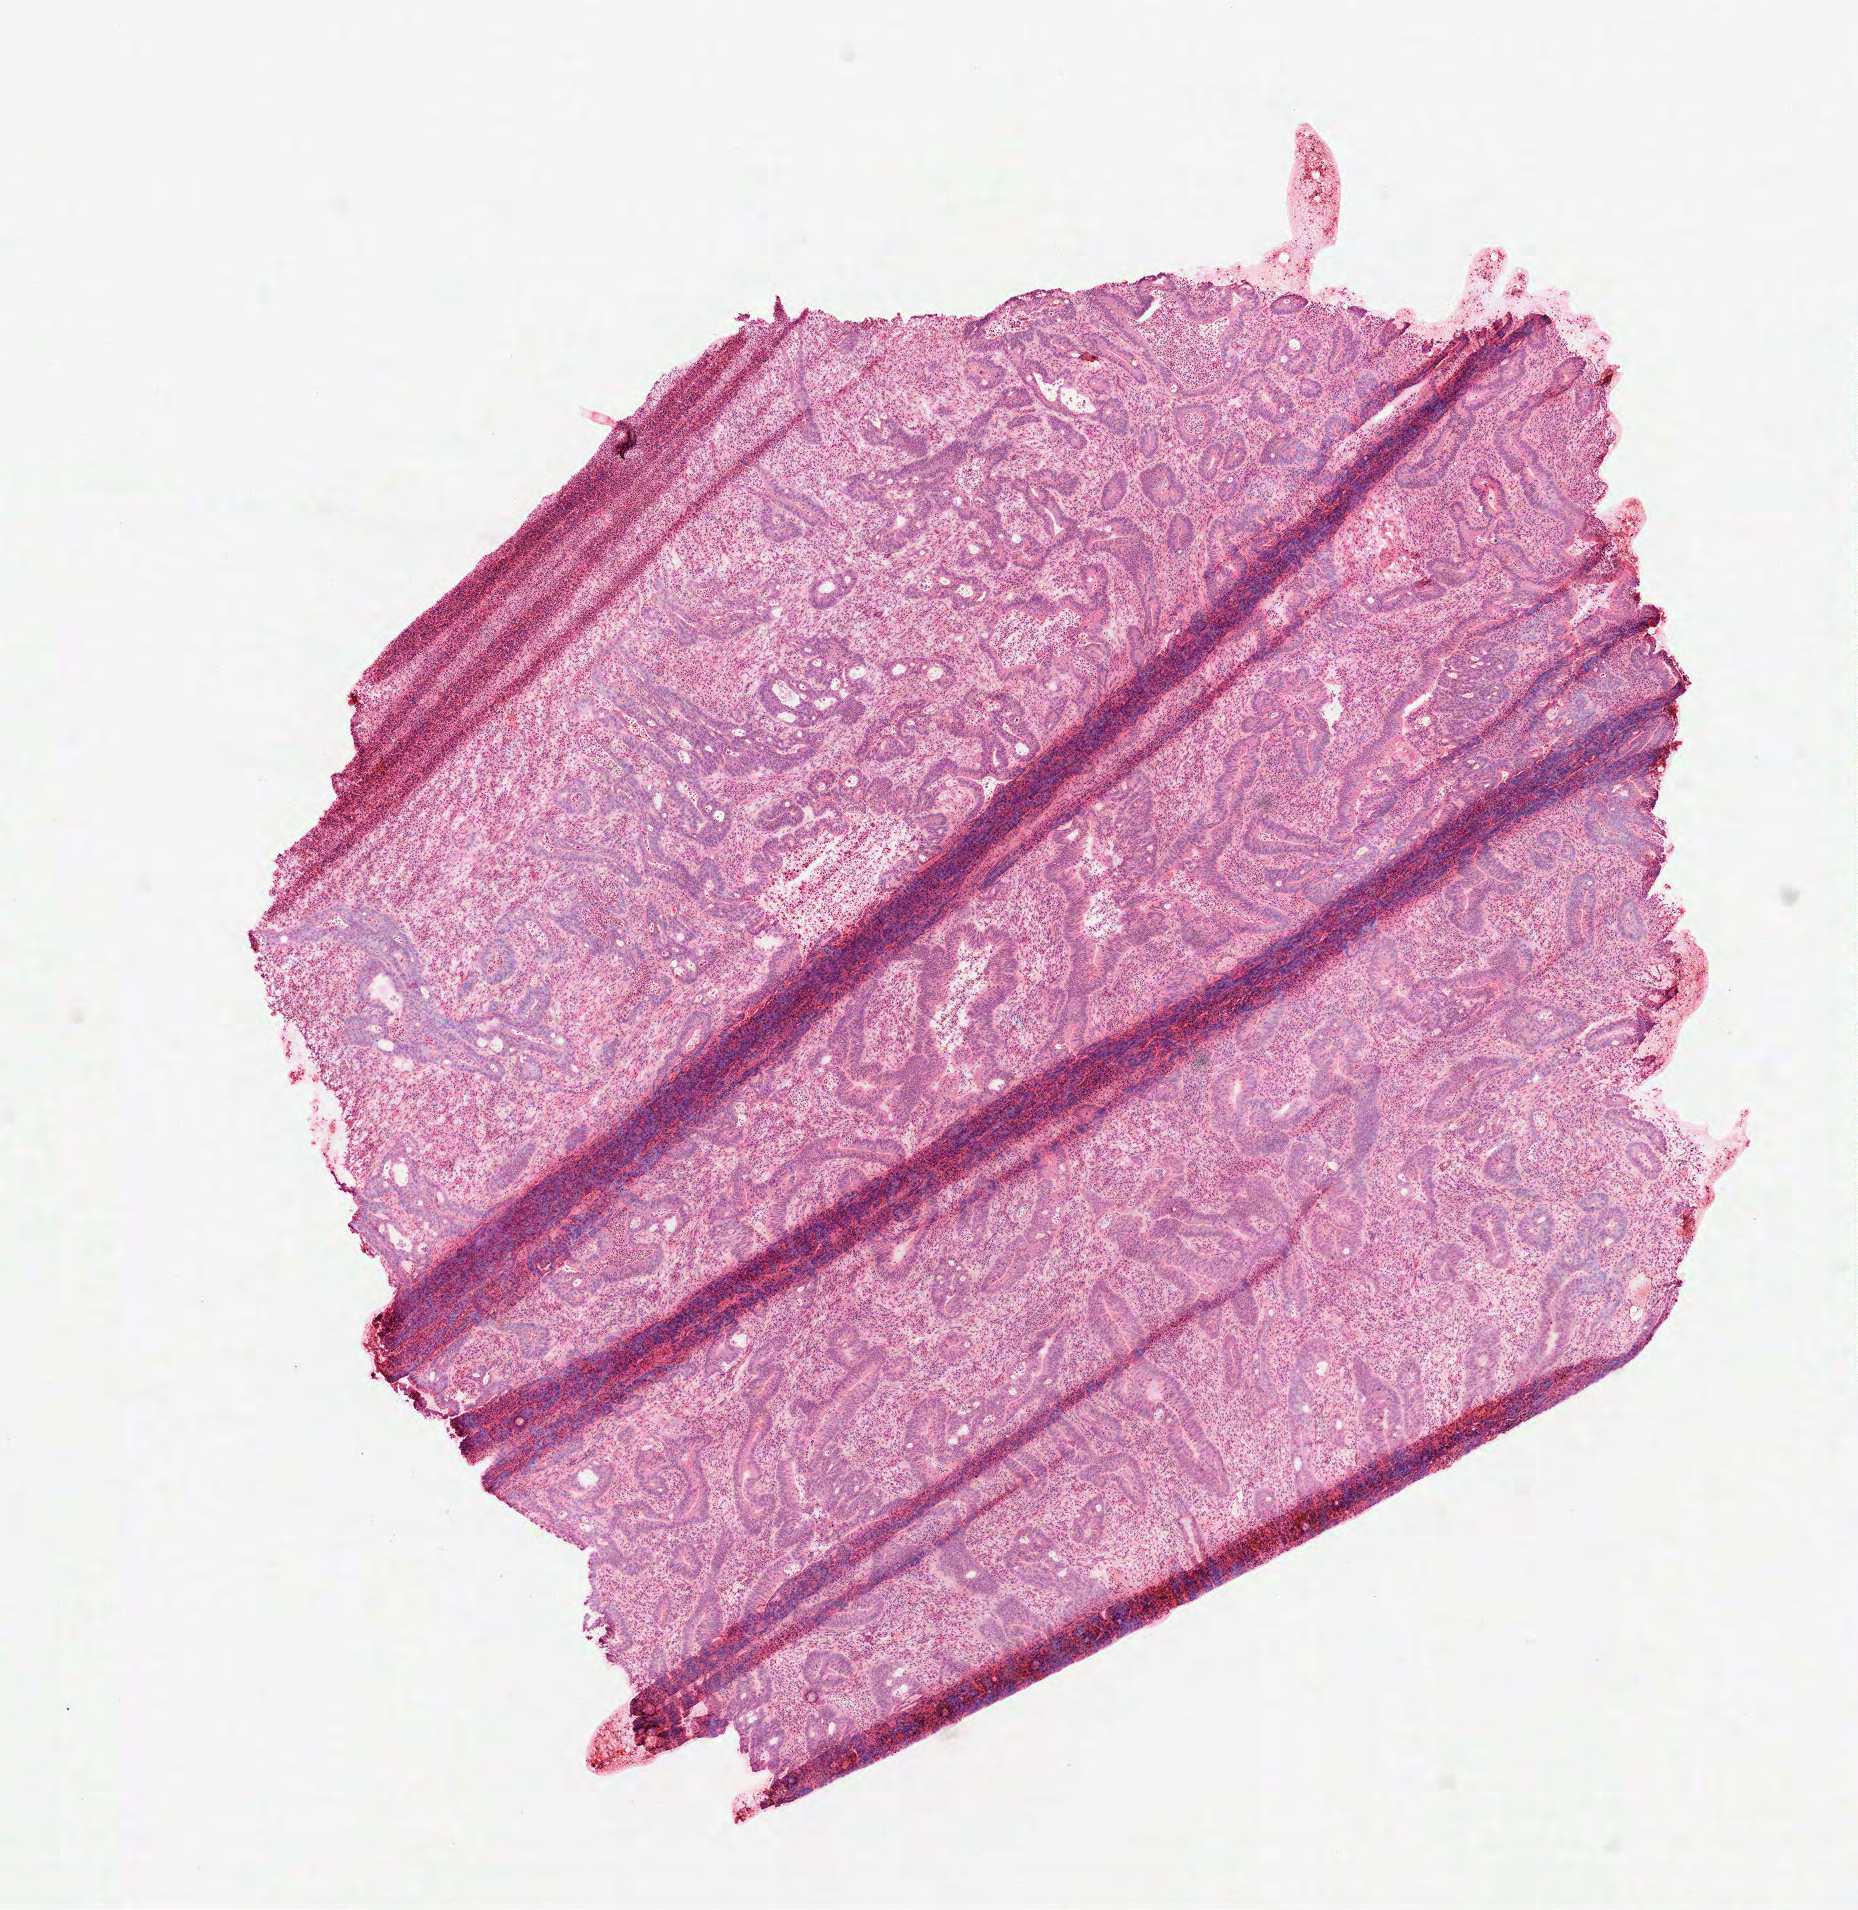
Digitized H&E tissue section (whole slide), low-resolution overview of the scanned area, about 7.5 x 7.7 mm. Frozen section from the top of the tissue portion. Sample: primary tumour, colon. Male, age 69 years at initial diagnosis. Pathologist review of this section (percent, as recorded): tumour cells 95%, tumour nuclei 71%, normal cells 0%, stromal cells 0%, necrosis 5%. Infiltration values recorded for this section: lymphocyte infiltration 15%, monocyte infiltration 0%, neutrophil infiltration 10%.
AJCC pathologic stage: IIA (7th edition). TNM: T3 N0 M0. Pathologic diagnosis: Adenocarcinoma, NOS.